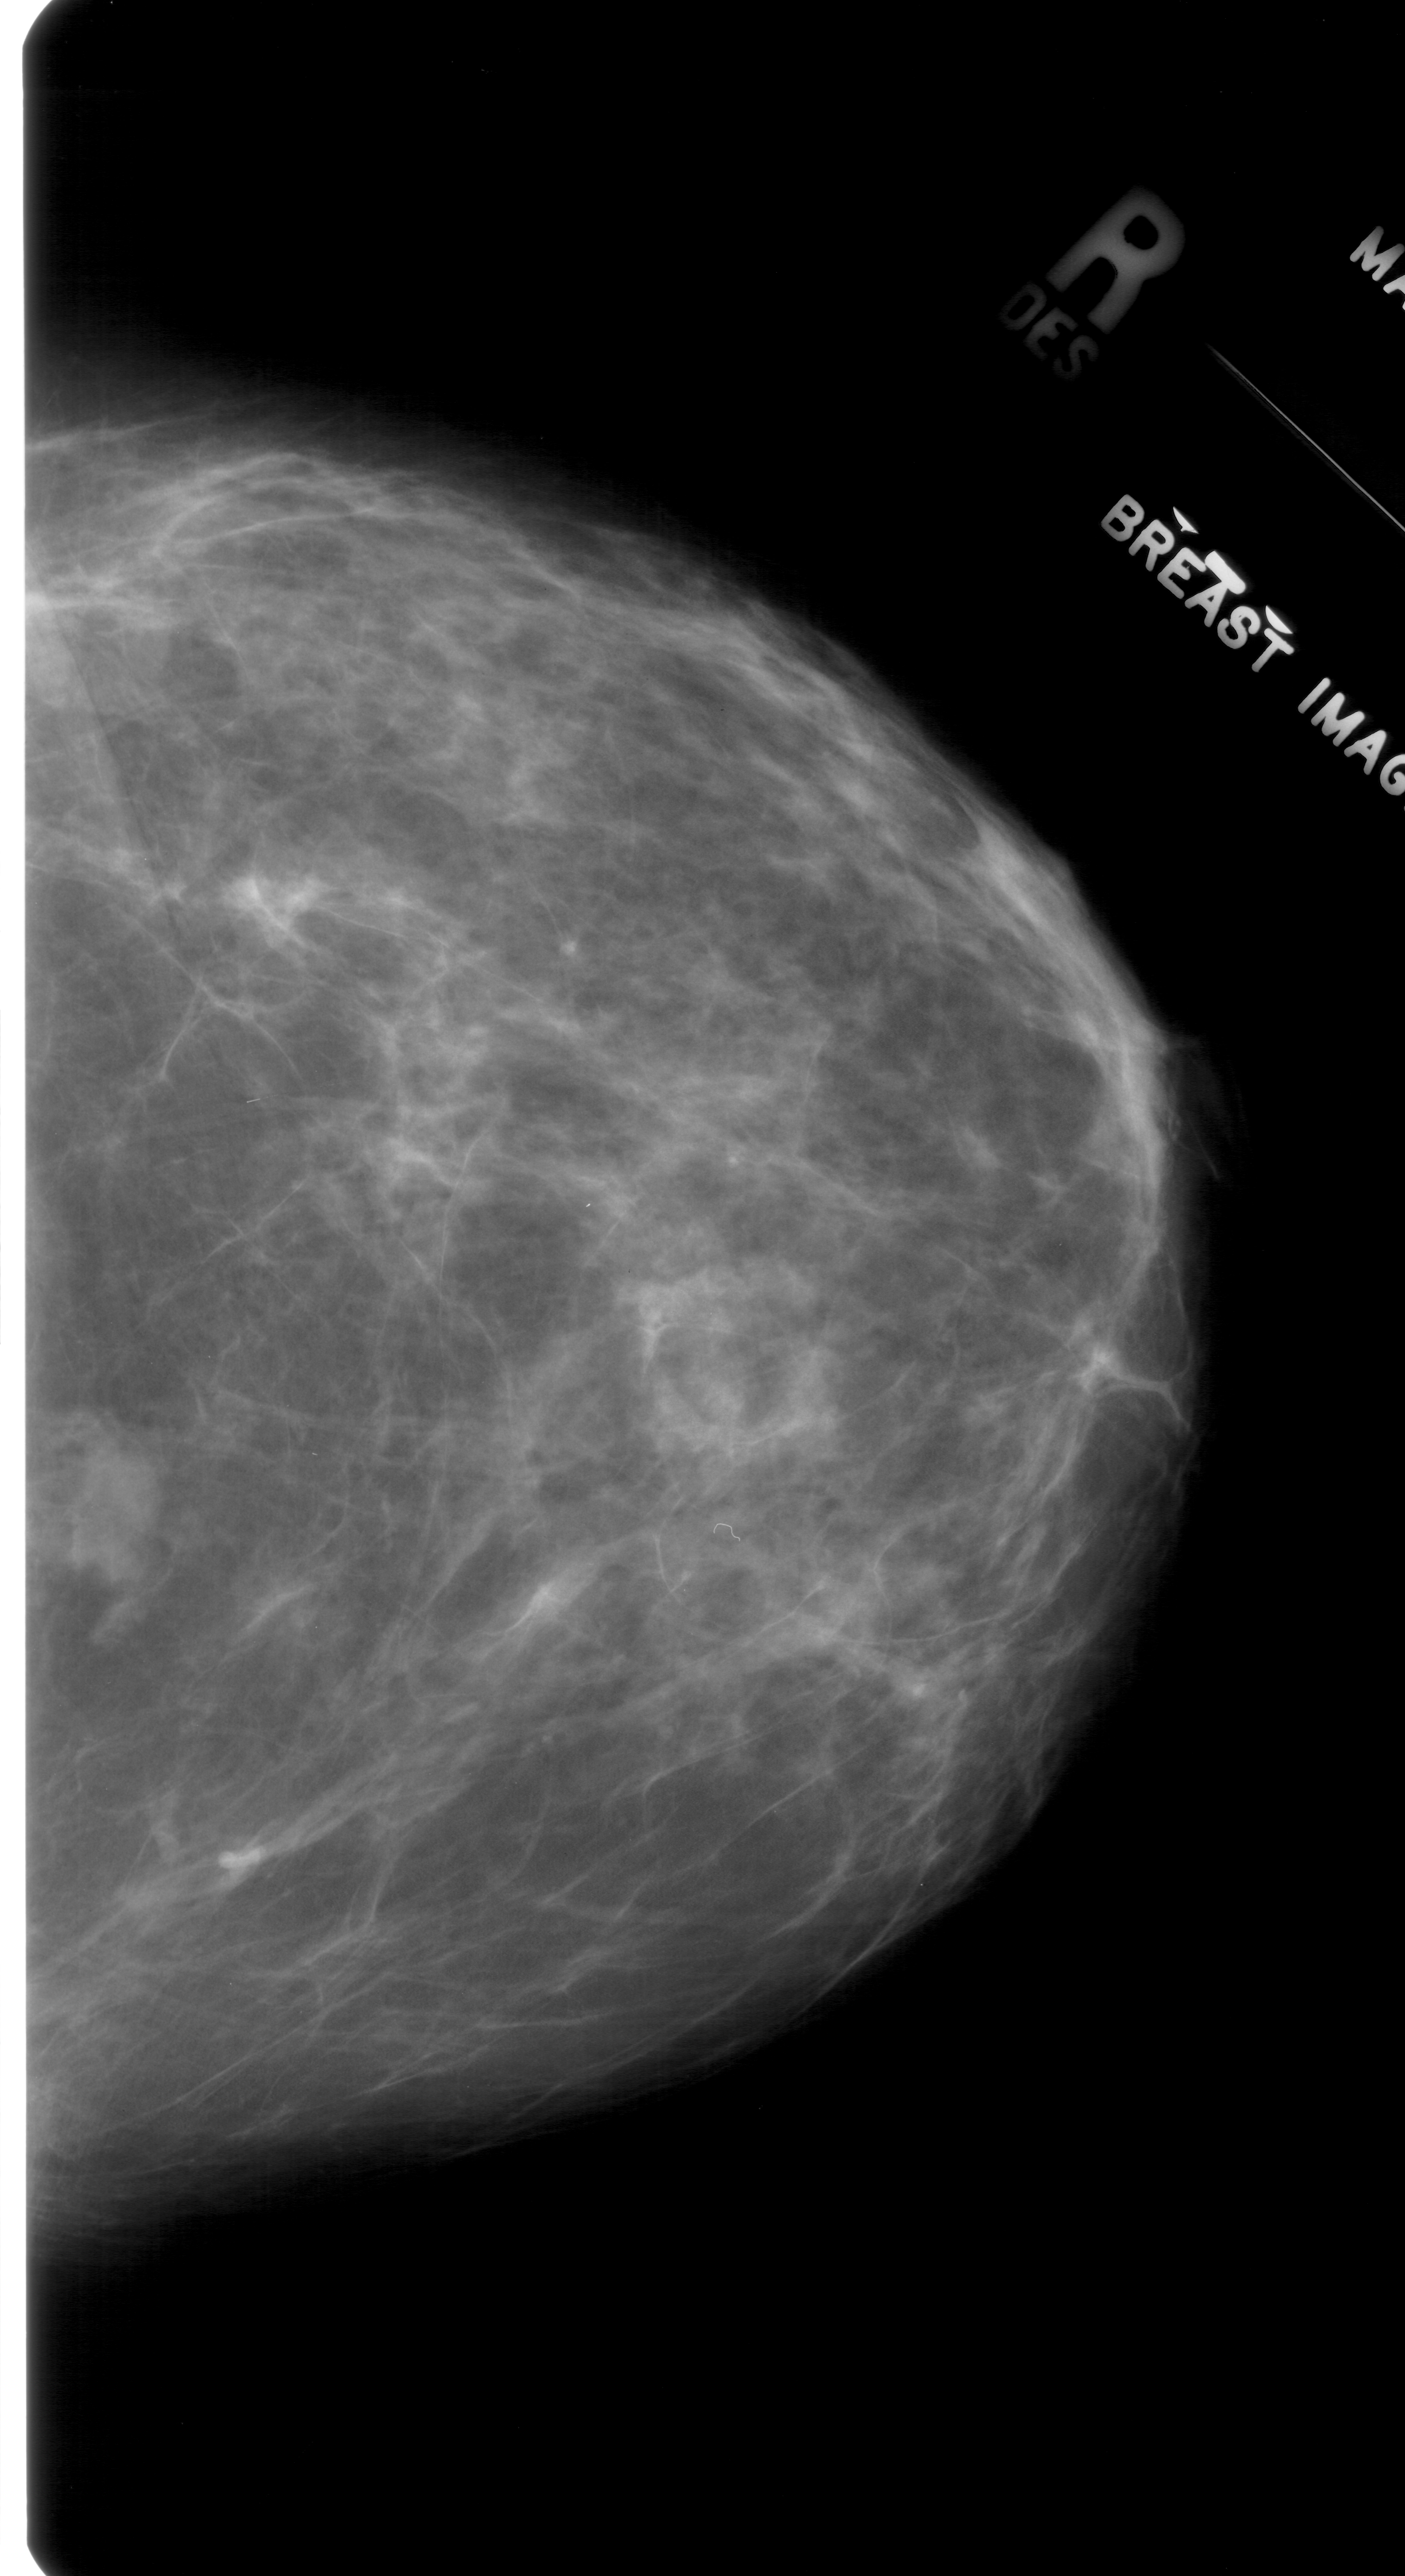
Digitized screen-film mammogram. Right breast. Craniocaudal (CC) view. BI-RADS breast density category 3 (scale 1–4). 1405 × 2576 image matrix.
Marked abnormalities (boxes around the expert regions of interest):
- mass, shape irregular, margins ill defined; BI-RADS assessment category 4; subtlety rating 2 on a 1 (subtle) to 5 (obvious) scale; pathology result (as recorded, not read from the image): benign: box from (x=30, y=1392) to (x=184, y=1592) px